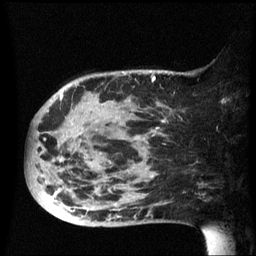
Breast MRI (dynamic contrast-enhanced), one sagittal slice; slice 20 of 60 in the series (ordered by position); dynamic contrast-enhanced series, image 2 of 3 at this slice position (ordered by acquisition); 1.5 T; TE 4.2 ms, TR 8.4 ms; 256 × 256 image matrix, field of view 220 × 220 mm. Patient: female, 49 years.
Annotated regions visible in this slice (semi-automatic segmentation, software-assisted and operator-edited):
- analysis volume of interest (the breast-tissue region the enhancement analysis was run in; not a lesion): bounding box <26,72,185,227> (left, top, right, bottom; pixels)
- tumour enhancement mask (voxels above the 70 % enhancement threshold inside the analysis volume of interest): <75,74,166,225>